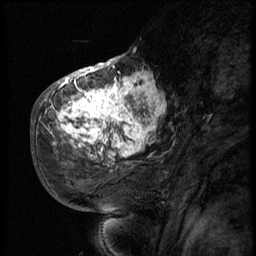
Breast MRI (dynamic contrast-enhanced), one sagittal slice. Slice 24 of 56 in the series (ordered by position). 3 images stored at this slice position (order not interpretable as contrast timing). 1.5 T. TE 4.2 ms, TR 9 ms. 256 × 256 image matrix, field of view 180 × 180 mm. Female patient, age 51 years. Case-level facts recorded for this patient, not image findings: setting: breast cancer imaged before/during neoadjuvant chemotherapy; receptor status: triple-negative.
Outlined on this slice (semi-automatic segmentation, software-assisted and operator-edited):
- analysis volume of interest (the breast-tissue region the enhancement analysis was run in; not a lesion): bounding box <52,66,170,179> (left, top, right, bottom; pixels)
- tumour enhancement mask (voxels above the 140 % enhancement threshold inside the analysis volume of interest): <52,66,166,161>